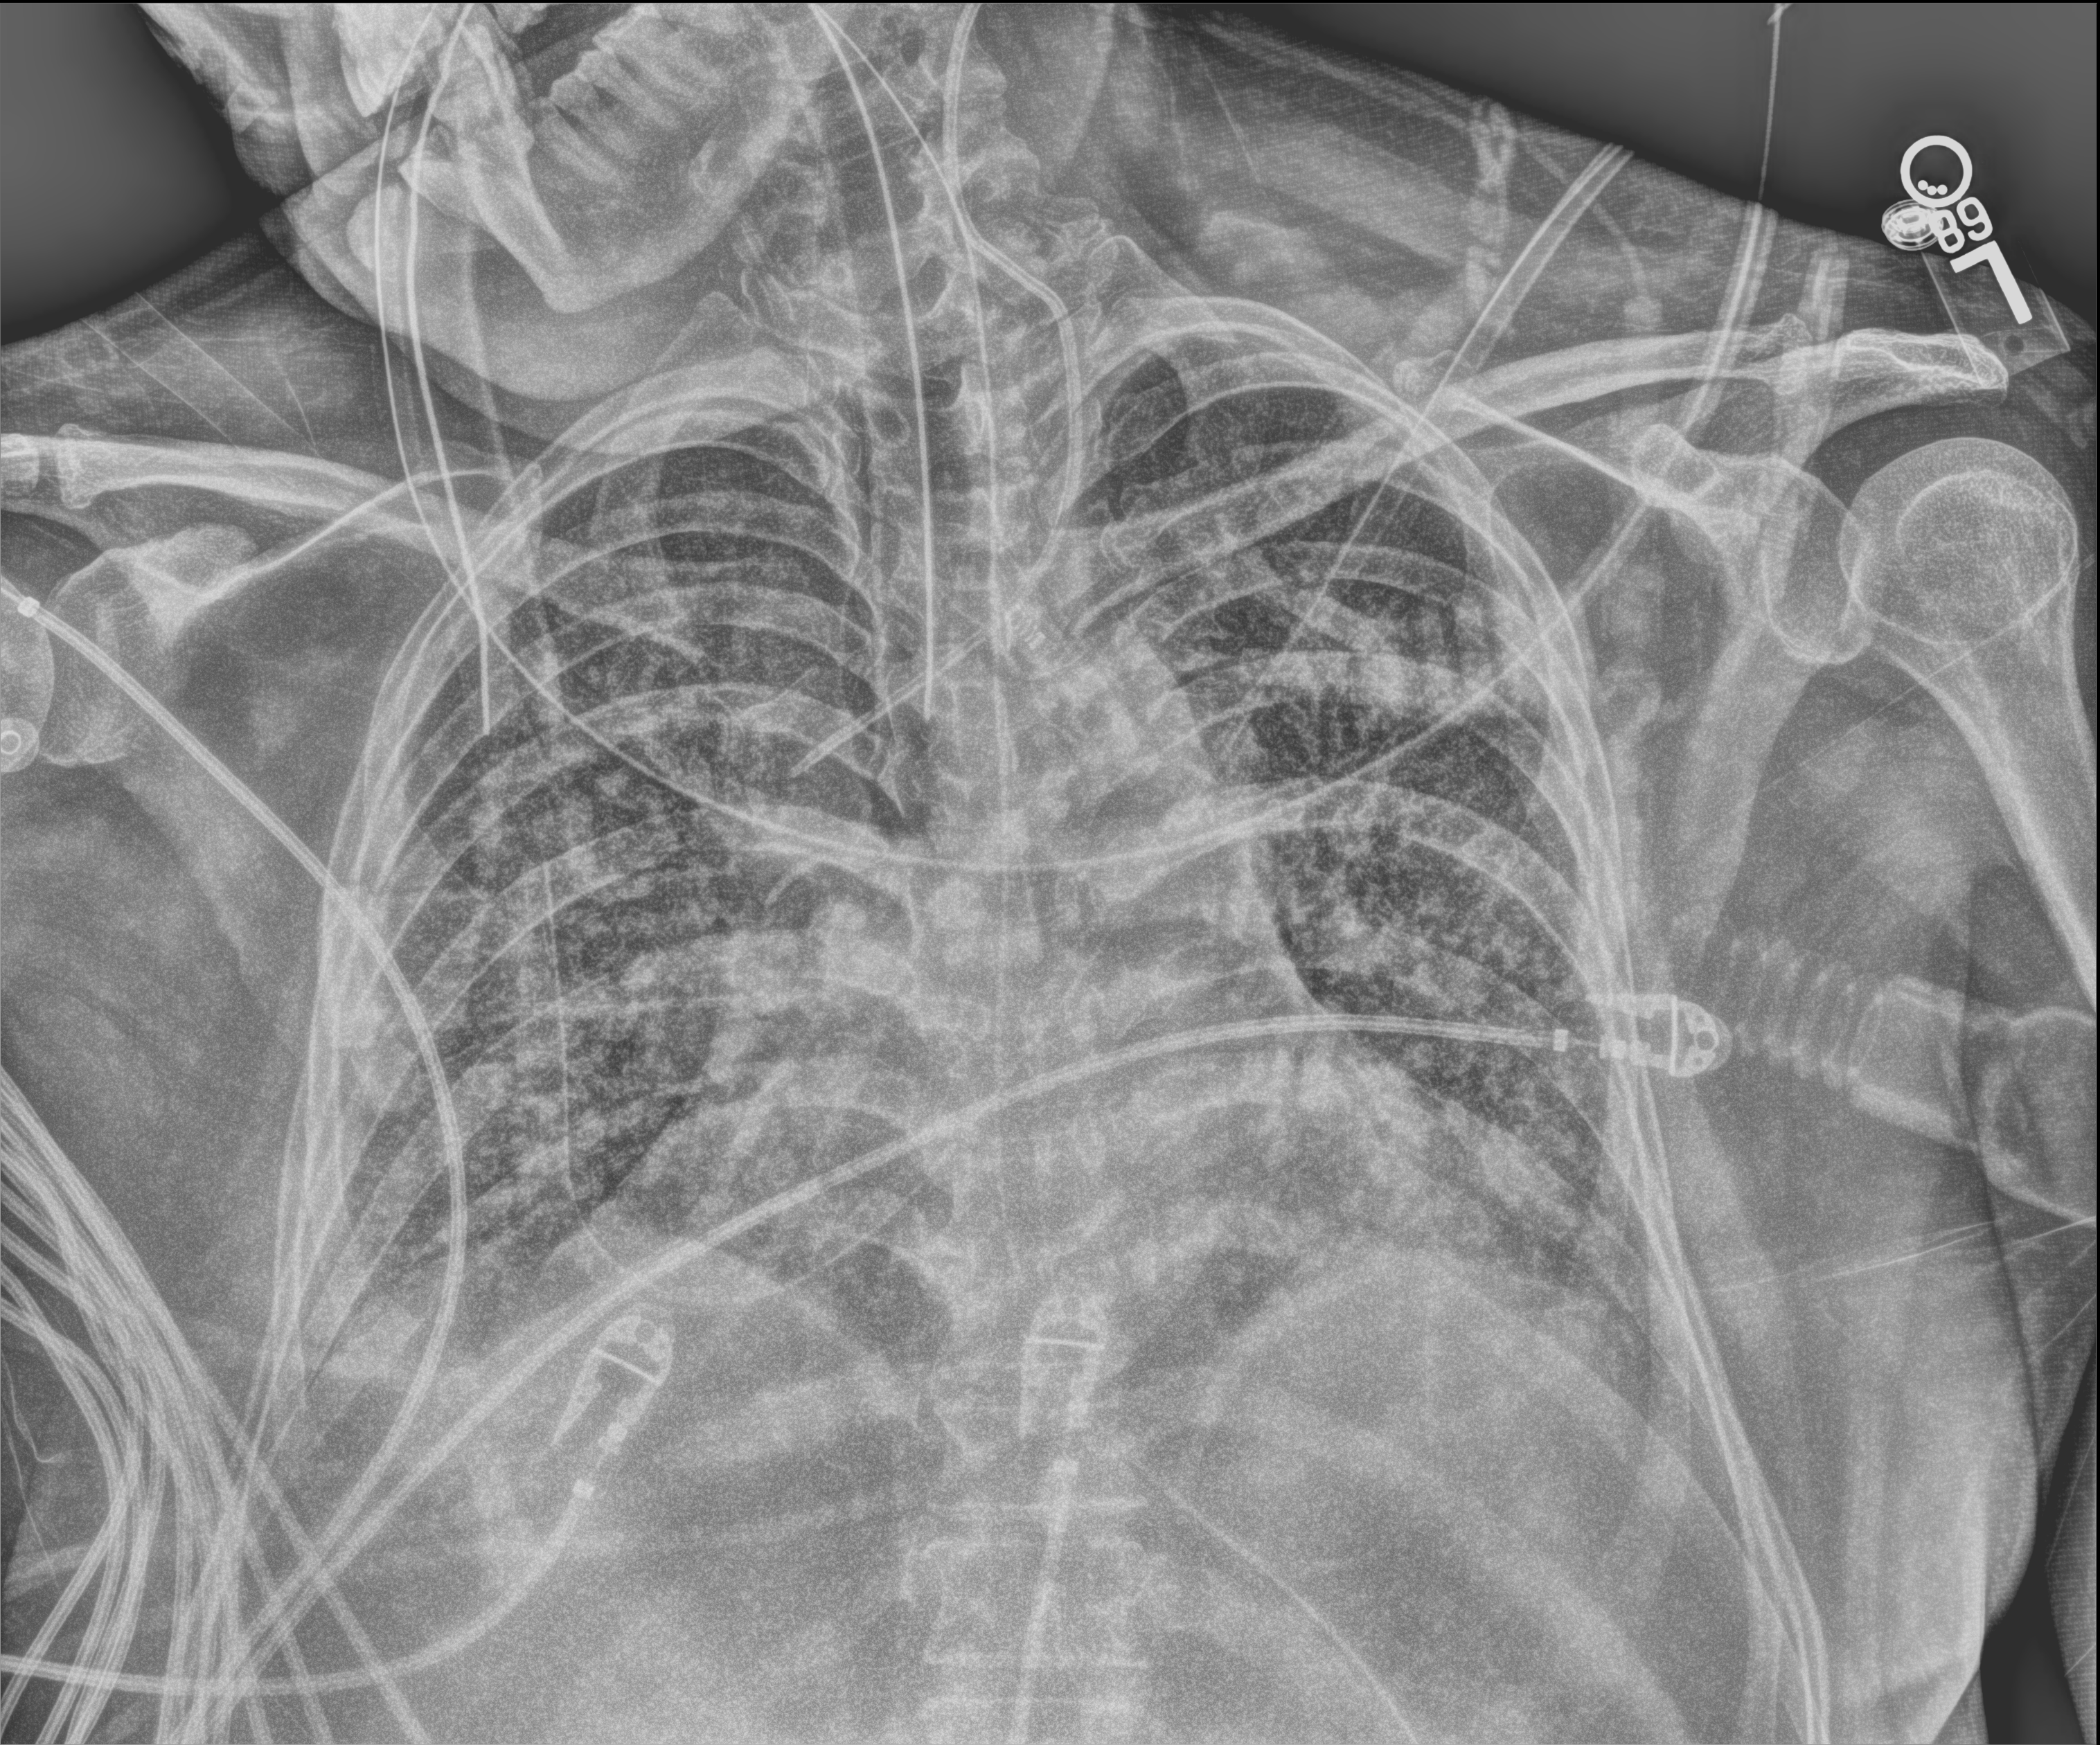
Bedside chest radiograph (digital radiography), anteroposterior (AP) projection. Patient hospitalised with COVID-19, aged 18–59 years.
From the hospital-stay record, not from the radiograph (when in the stay this image was taken is not recorded):
- admitted to intensive care during this hospital stay: yes
- mechanically ventilated during this hospital stay: yes
- length of hospital stay: 48 days